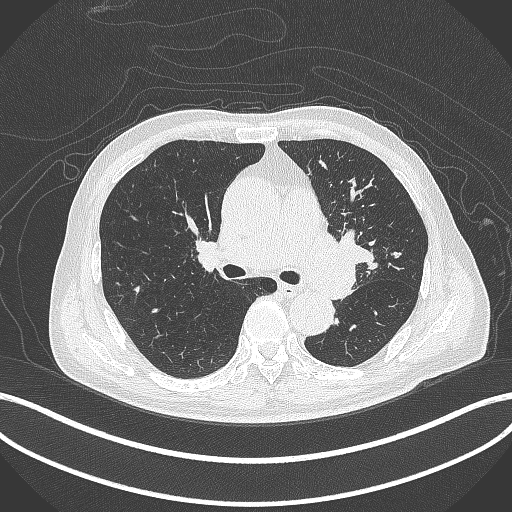
Chest CT, one axial slice; position 261 of 417 along the scan axis; reconstruction kernel B70f; lung window (W 1500 / L -600 HU); 1 mm slice thickness; 512 × 512 image matrix. Male patient, age 77 years. From the clinical record (not read from this slice): clinical TNM (as recorded): T3 N1 M0.
Annotated regions visible in this slice (bounding box drawn by a radiologist):
- lung tumour (recorded histology: adenocarcinoma): box from (x=311, y=222) to (x=371, y=298) px